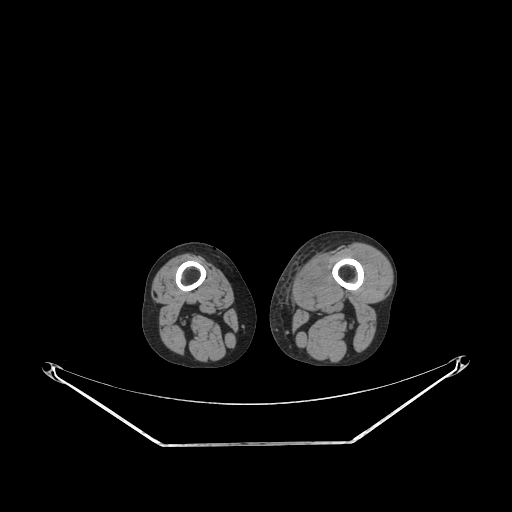
CT of an extremity soft-tissue mass (from a PET/CT study), one axial slice. Position 206 of 267 along the scan axis. 140 kVp. Soft-tissue window (W 400 / L 40 HU). 3.75 mm slice thickness. 512 × 512 image matrix. Male patient. From the clinical record (not read from this slice): histological type: pleiomorphic leiomyosarcoma; grade: high; site of the primary tumour: left thigh.
Annotated regions visible in this slice (expert contour drawn on MRI and transferred to this co-registered scan by the dataset authors):
- gross tumour volume including surrounding oedema: bounding box [x1, y1, x2, y2] px = [295, 253, 328, 305]